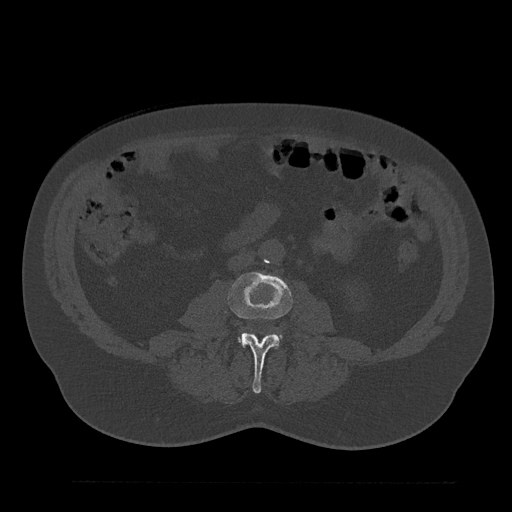
CT including the spine, one axial slice. Position 15 of 797 along the scan axis. 120 kVp. Bone window (W 1800 / L 400 HU). 0.5 mm slice thickness. 512 × 512 image matrix, field of view 430 × 430 mm. Patient: male, 61 years. From the clinical record (not read from this slice): primary cancer: prostate.
Outlined on this slice (semi-automatic segmentation, software-assisted and operator-edited):
- L3 vertebra: box from (x=228, y=272) to (x=292, y=394) px
- L4 vertebra: (x=240, y=338)–(x=243, y=344)